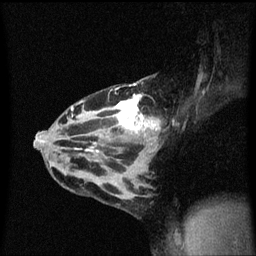
Breast MRI (dynamic contrast-enhanced), one sagittal slice. Position 34 of 60 along the scan axis. Dynamic contrast-enhanced series, image 2 of 3 at this slice position (ordered by acquisition). 1.5 T. TE 4.2 ms, TR 8.4 ms. 2 mm slice thickness. 256 × 256 image matrix, field of view 200 × 200 mm. Patient: female, 32 years.
Annotated regions visible in this slice (semi-automatically segmented with operator editing):
- analysis volume of interest (the breast-tissue region the enhancement analysis was run in; not a lesion): bounding box (x1, y1, x2, y2) in pixels: (55, 78, 166, 167)
- tumour enhancement mask (voxels above the 70 % enhancement threshold inside the analysis volume of interest): (72, 84, 160, 153)